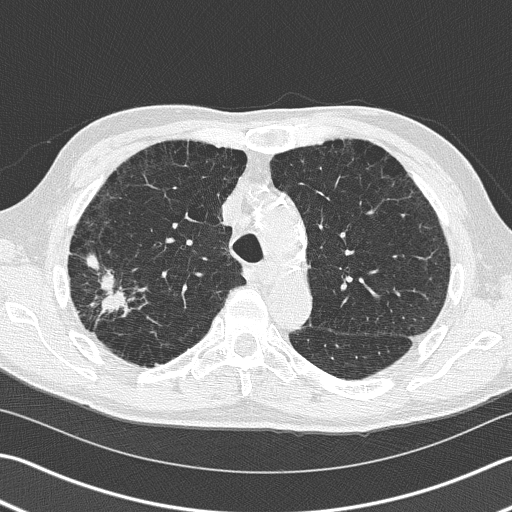
Low-dose screening chest CT, one axial slice. Slice 112 of 163 in the series (ordered by position). Reconstruction kernel B50f. Lung window (W 1500 / L -600 HU). 512 × 512 image matrix.
Outlined on this slice (manually delineated by an expert):
- lesion 1 (tumor, upper lobe of right lung): box from (x=87, y=254) to (x=129, y=314) px